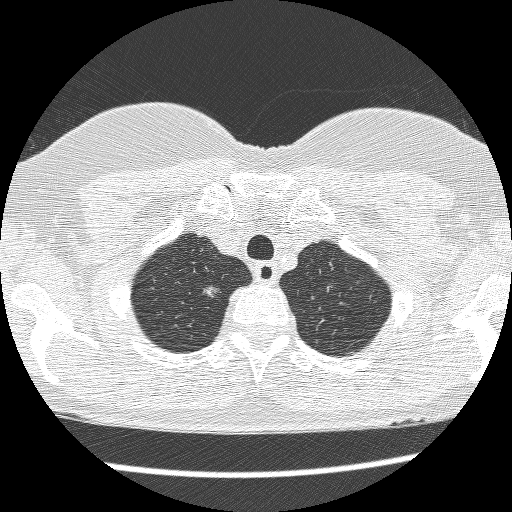
Axial slice from a low-dose chest CT screening exam. Baseline screening round. Lung window (W 1500 / L -600 HU). Lung (sharp) reconstruction kernel (BONE). Slice 204 of 227 in the series. Female, age 61 years at enrolment.
Lesion marked by an expert reader, bounding box [x1, y1, x2, y2] px = [194, 280, 228, 306]. The exam's reader record, not a measurement of the box and not confirmed to be the same lesion: non-calcified nodule or mass ≥4 mm, right upper lobe, 7 × 6 mm, poorly defined margins, mixed attenuation. Later outcome: lung cancer diagnosed 403 days after this screen (after the second annual screen) — adenocarcinoma, NOS, right upper lobe, poorly differentiated (G3), 12 mm at pathology.